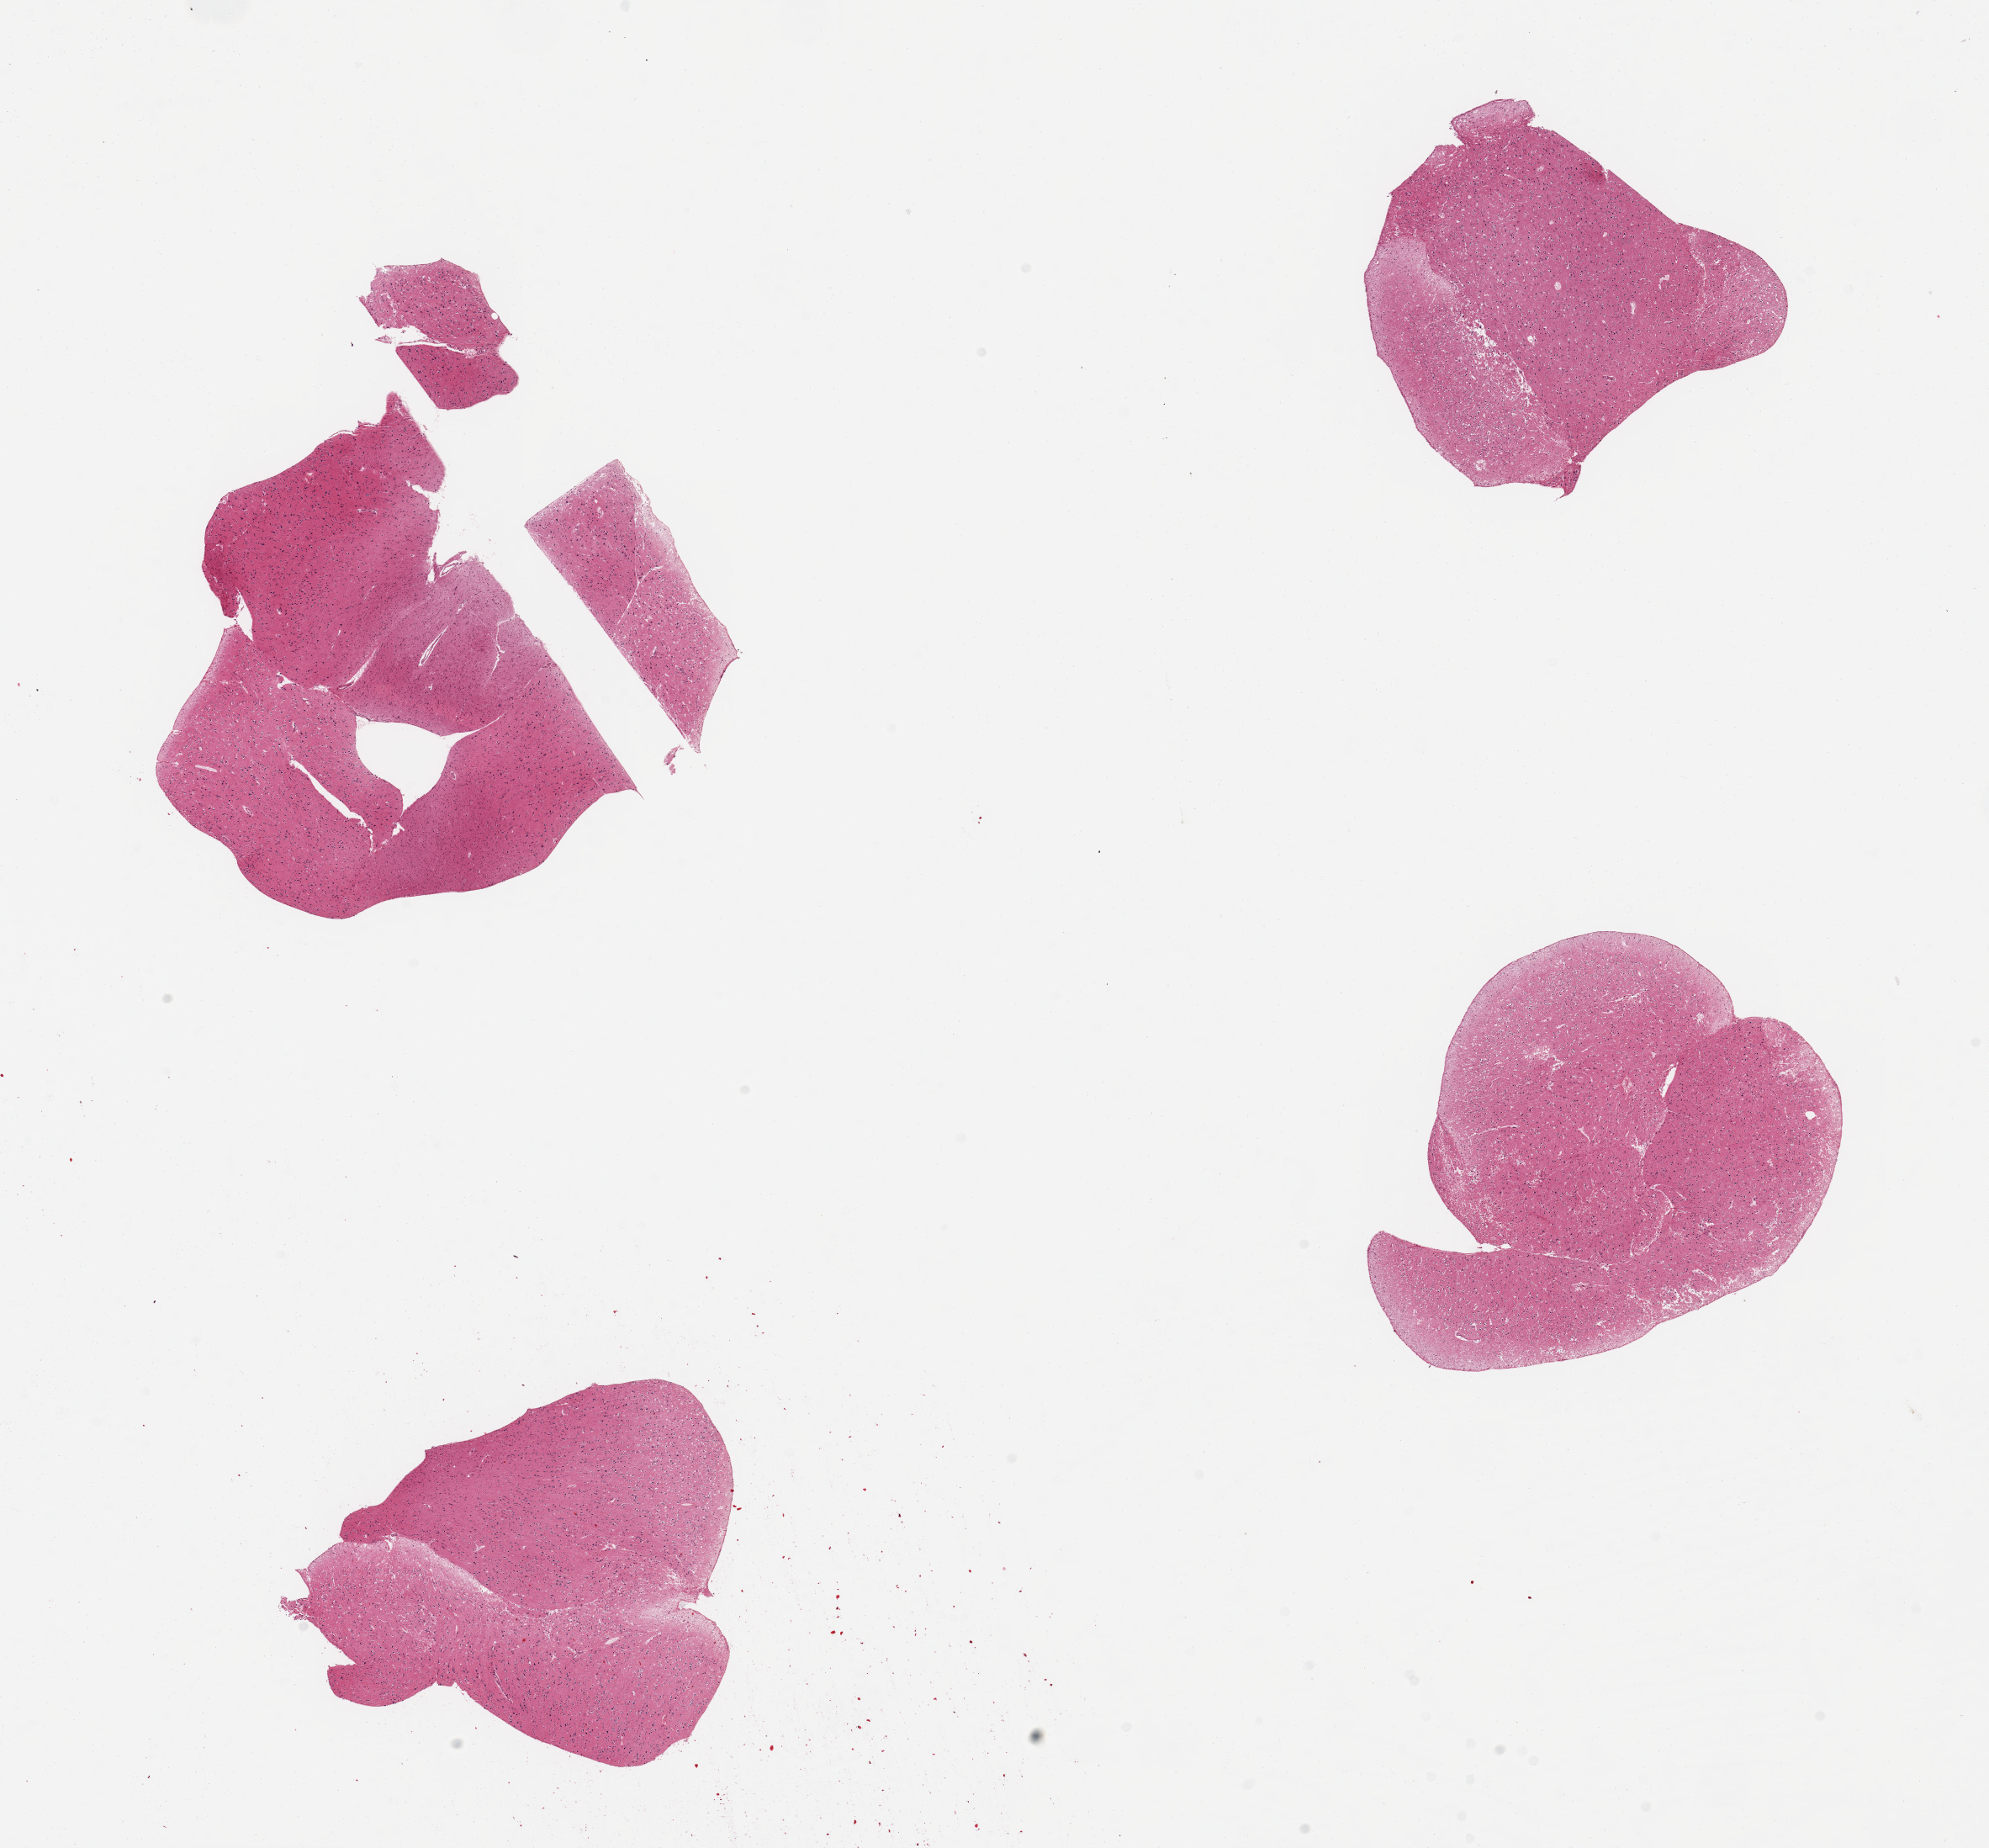
H&E whole-slide image, brightfield — shown as a low-resolution overview of the whole scanned area (about 18.7 x 17.4 mm), PAXgene-fixed paraffin-embedded (PFPE) section, target tissue: cerebral cortex, donor tissue sample. Donor sex: female.
• review note (as recorded): 4 pieces